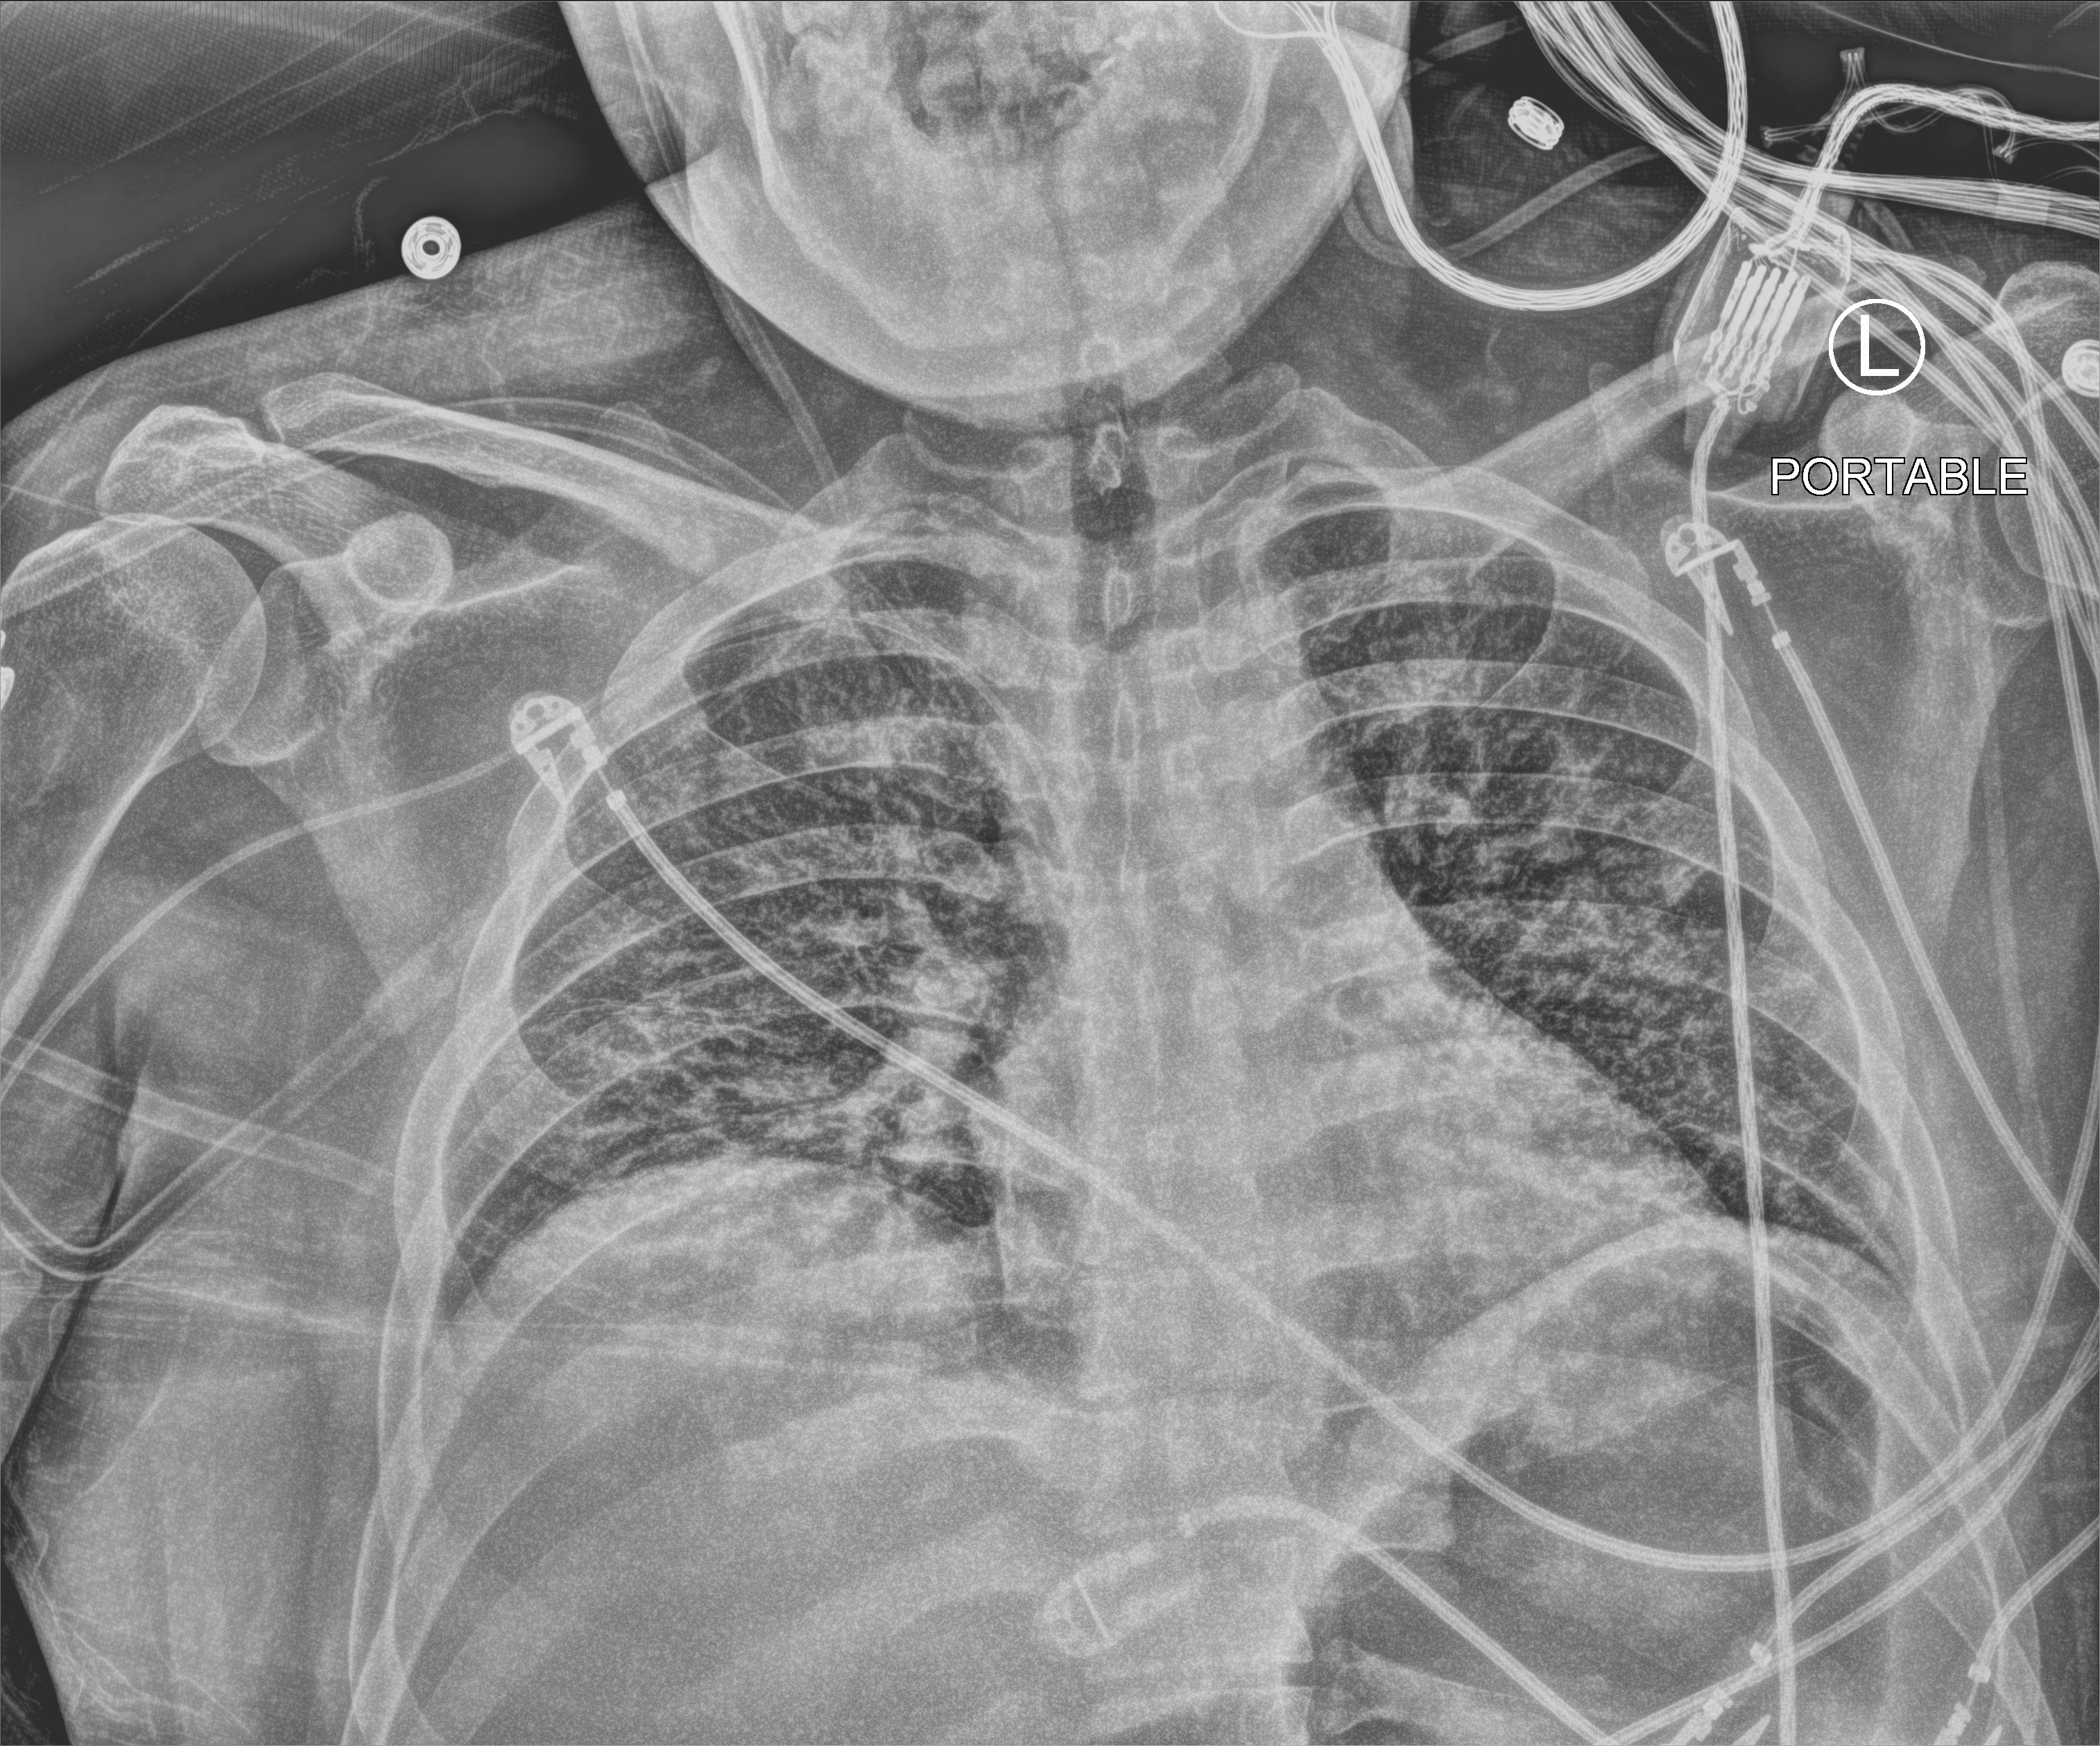
Portable chest radiograph, anteroposterior (AP) projection. Male patient hospitalised with COVID-19, age 18–59 years.
Admission-level facts for this patient (not findings on this image; timing relative to this image not recorded): mechanically ventilated during this hospital stay: yes; admitted to intensive care during this hospital stay: yes.